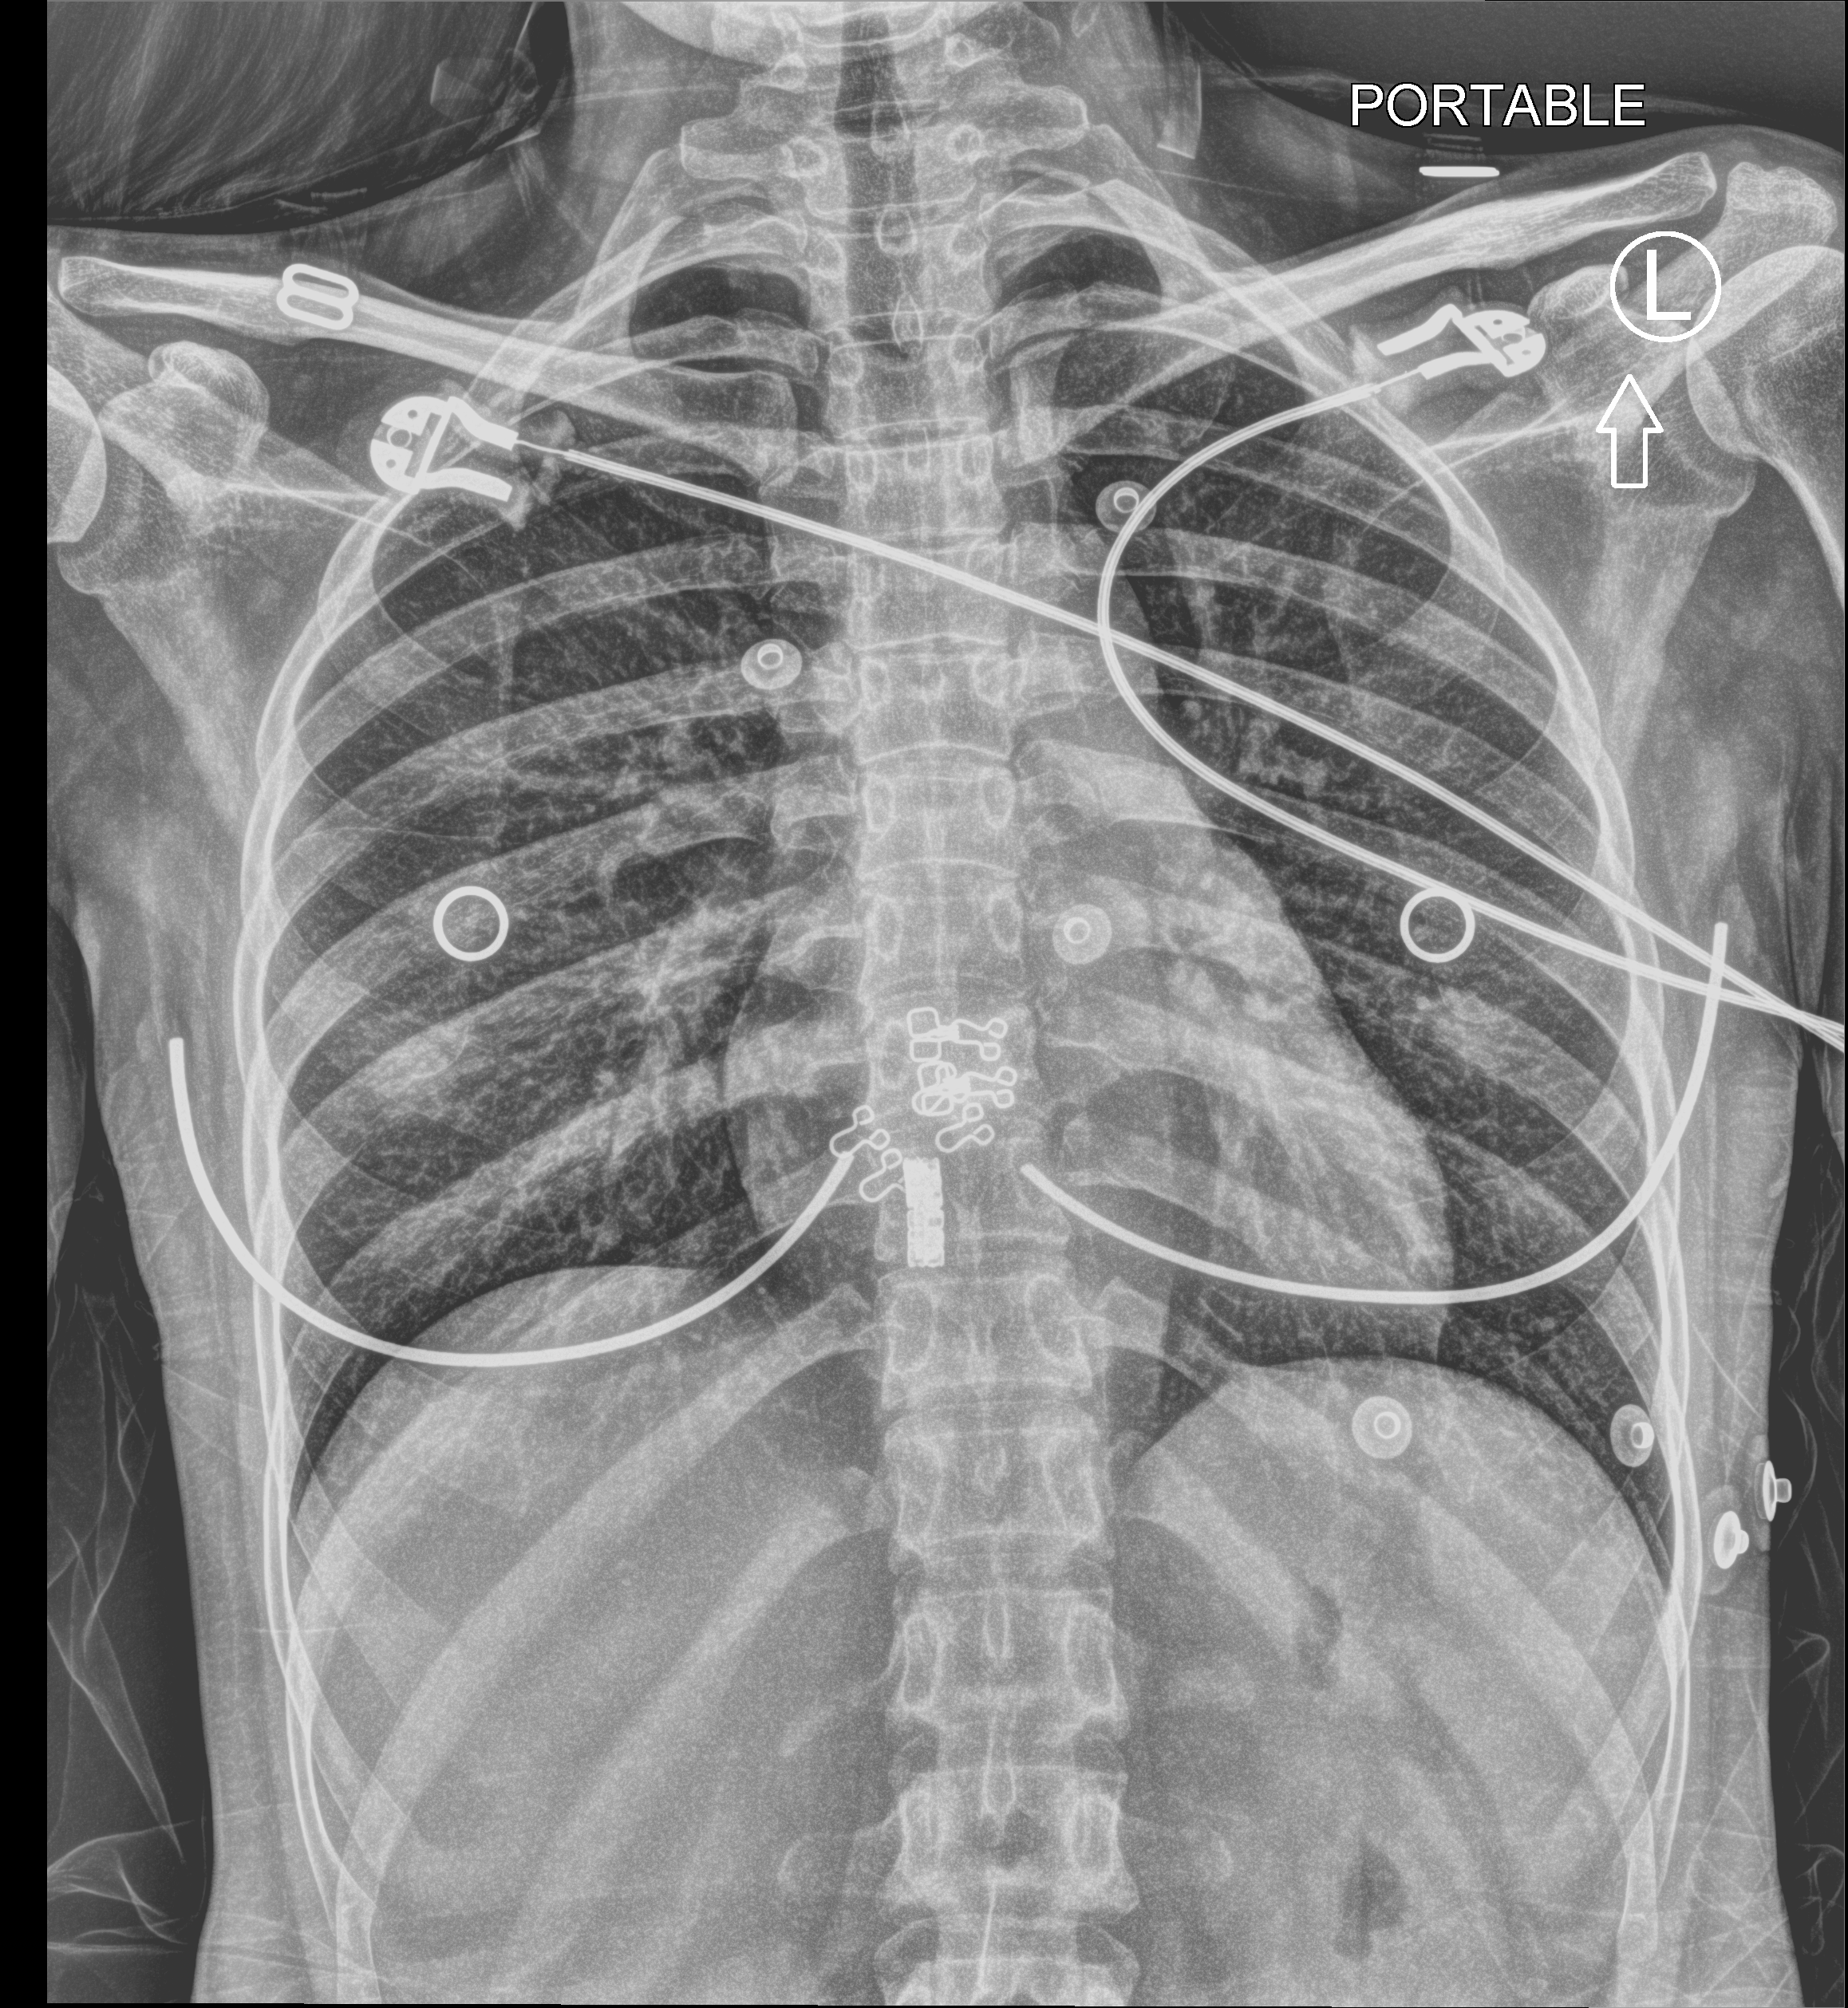
Chest X-ray (portable); anteroposterior (AP) projection. Female patient hospitalised with COVID-19, age 18–59 years.
From the hospital-stay record, not from the radiograph (when in the stay this image was taken is not recorded):
- COPD (admission record): no
- mechanically ventilated during this hospital stay: no
- admitted to intensive care during this hospital stay: no